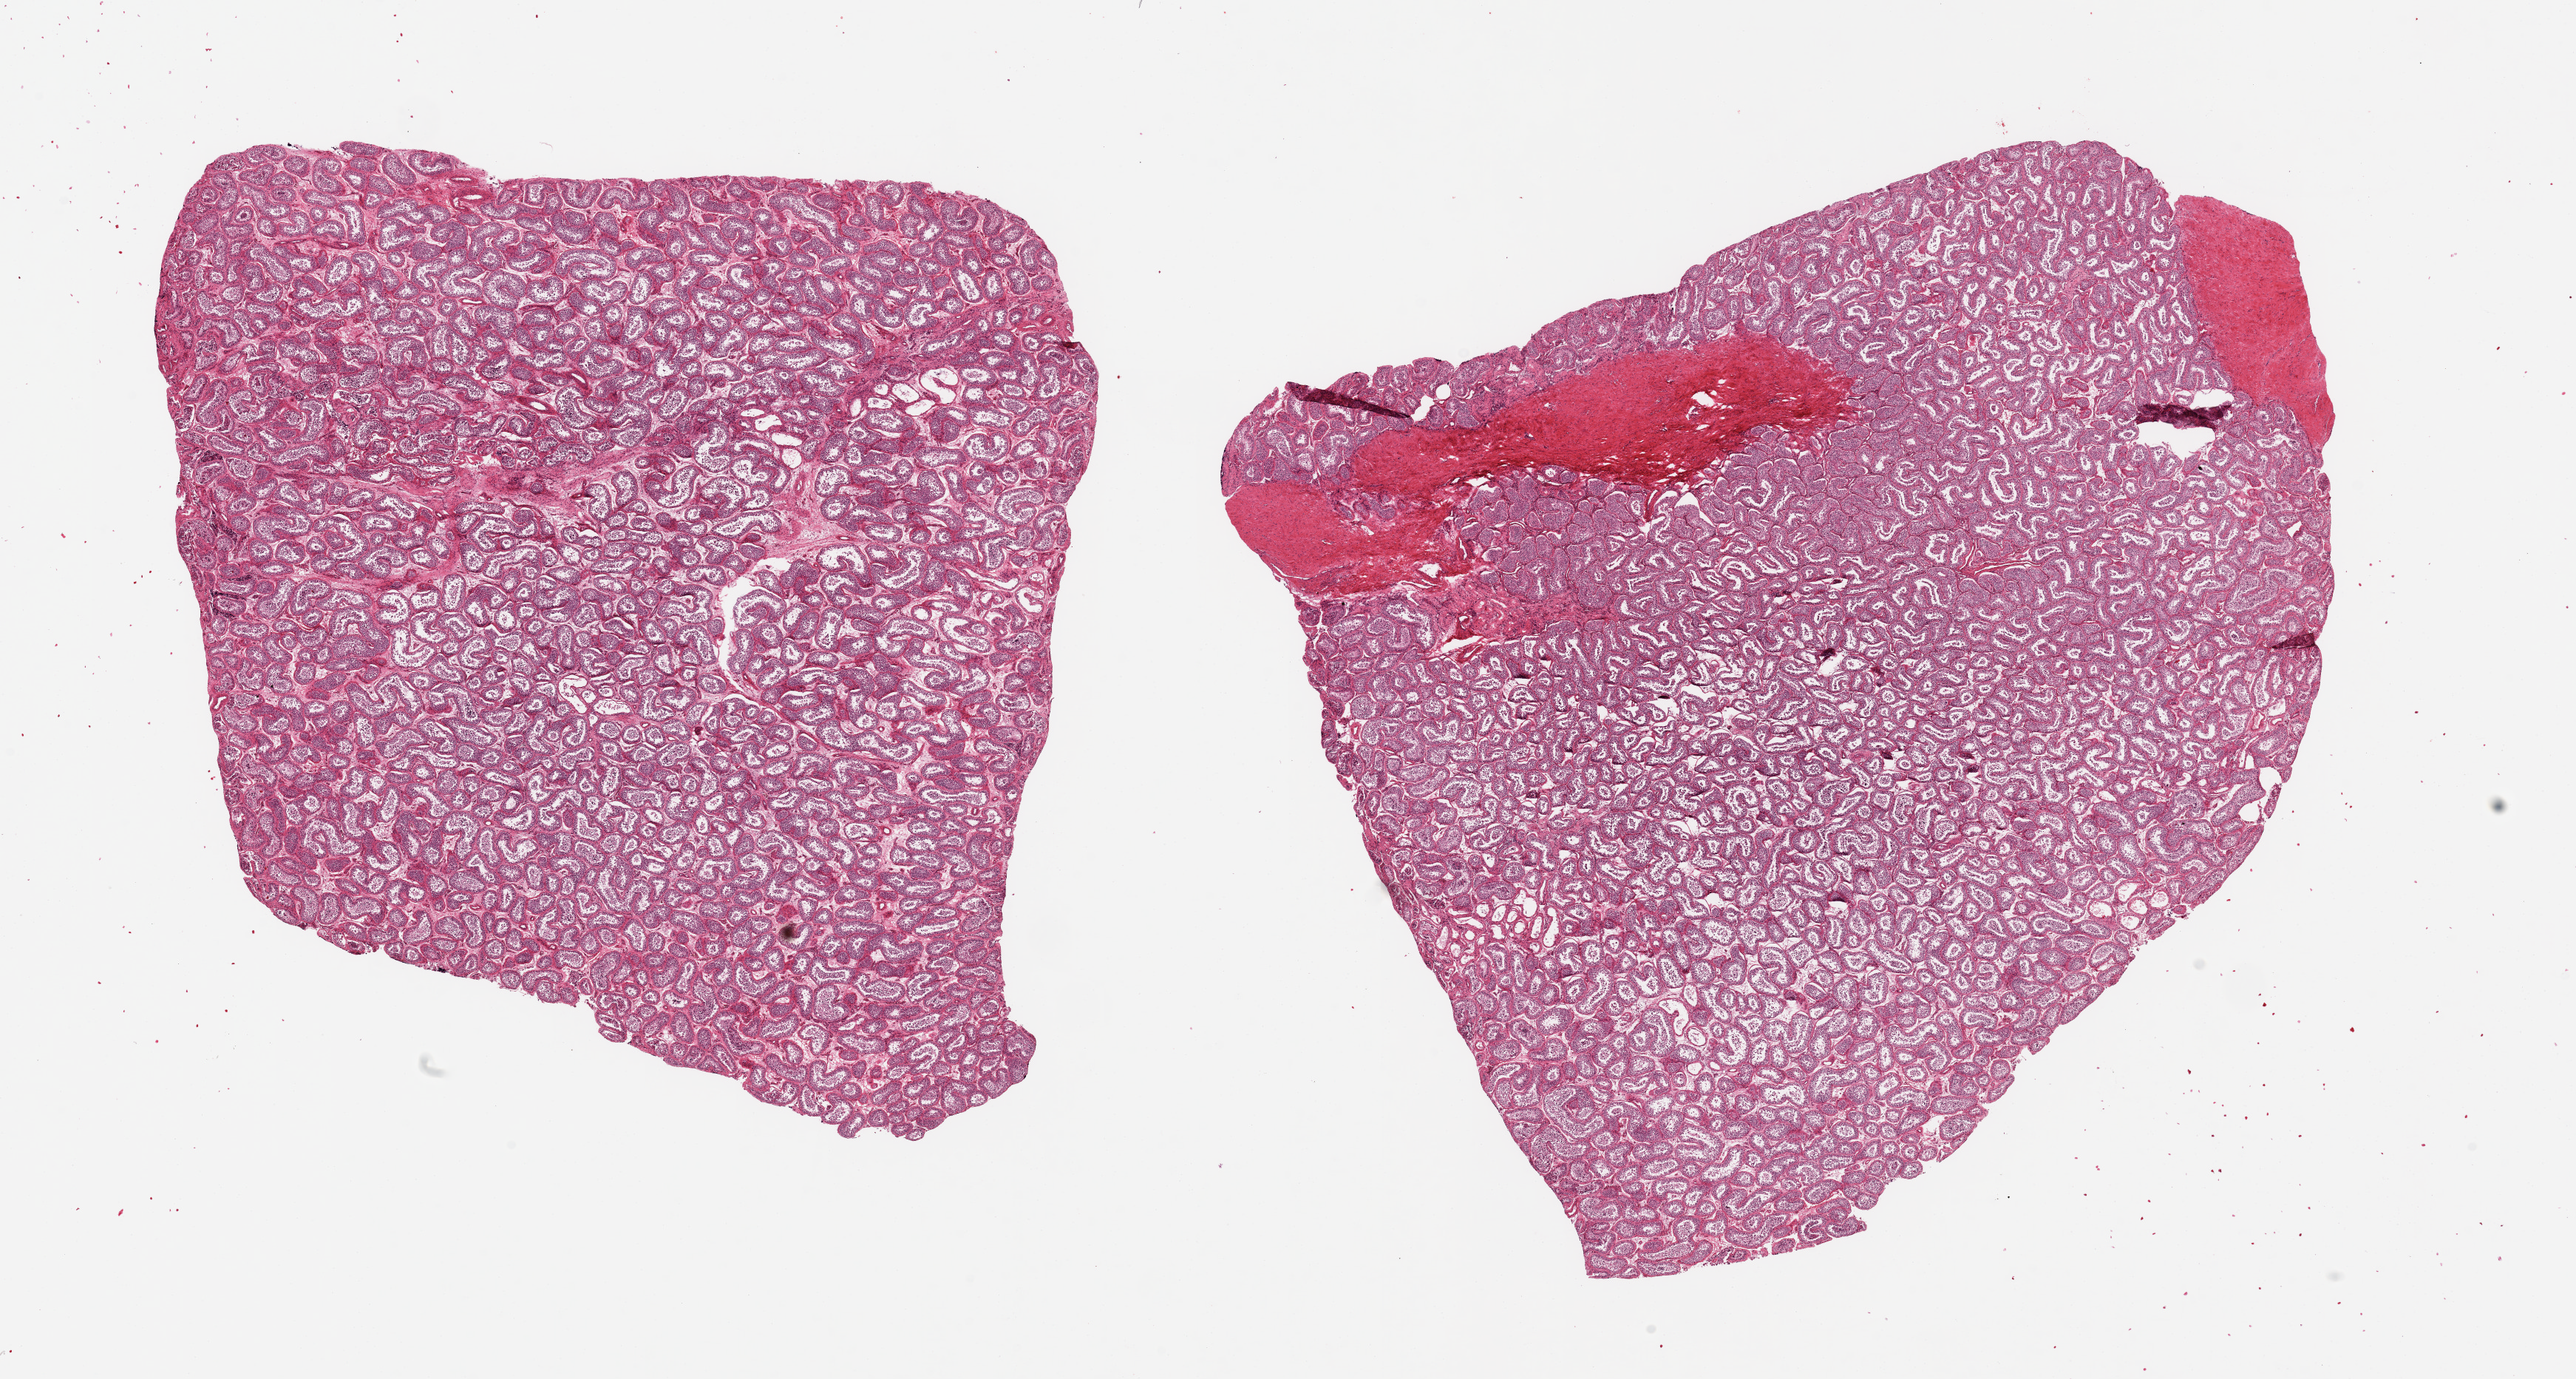
Haematoxylin and eosin whole-slide image, shown as a low-resolution overview of the whole scanned area (about 27.6 x 14.8 mm). PAXgene-fixed paraffin-embedded (PFPE) section. Target tissue: testis. Tissue donor sample. Donor sex: male.
Pathologist's review note for this sample: 2 pieces ~10x9mm.